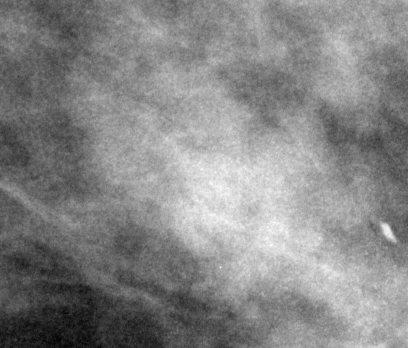
Crop from a digitized film mammogram around one marked abnormality, right breast, MLO view.
Mass, shape irregular, margins ill defined; BI-RADS assessment category 4; pathology (as recorded): malignant.